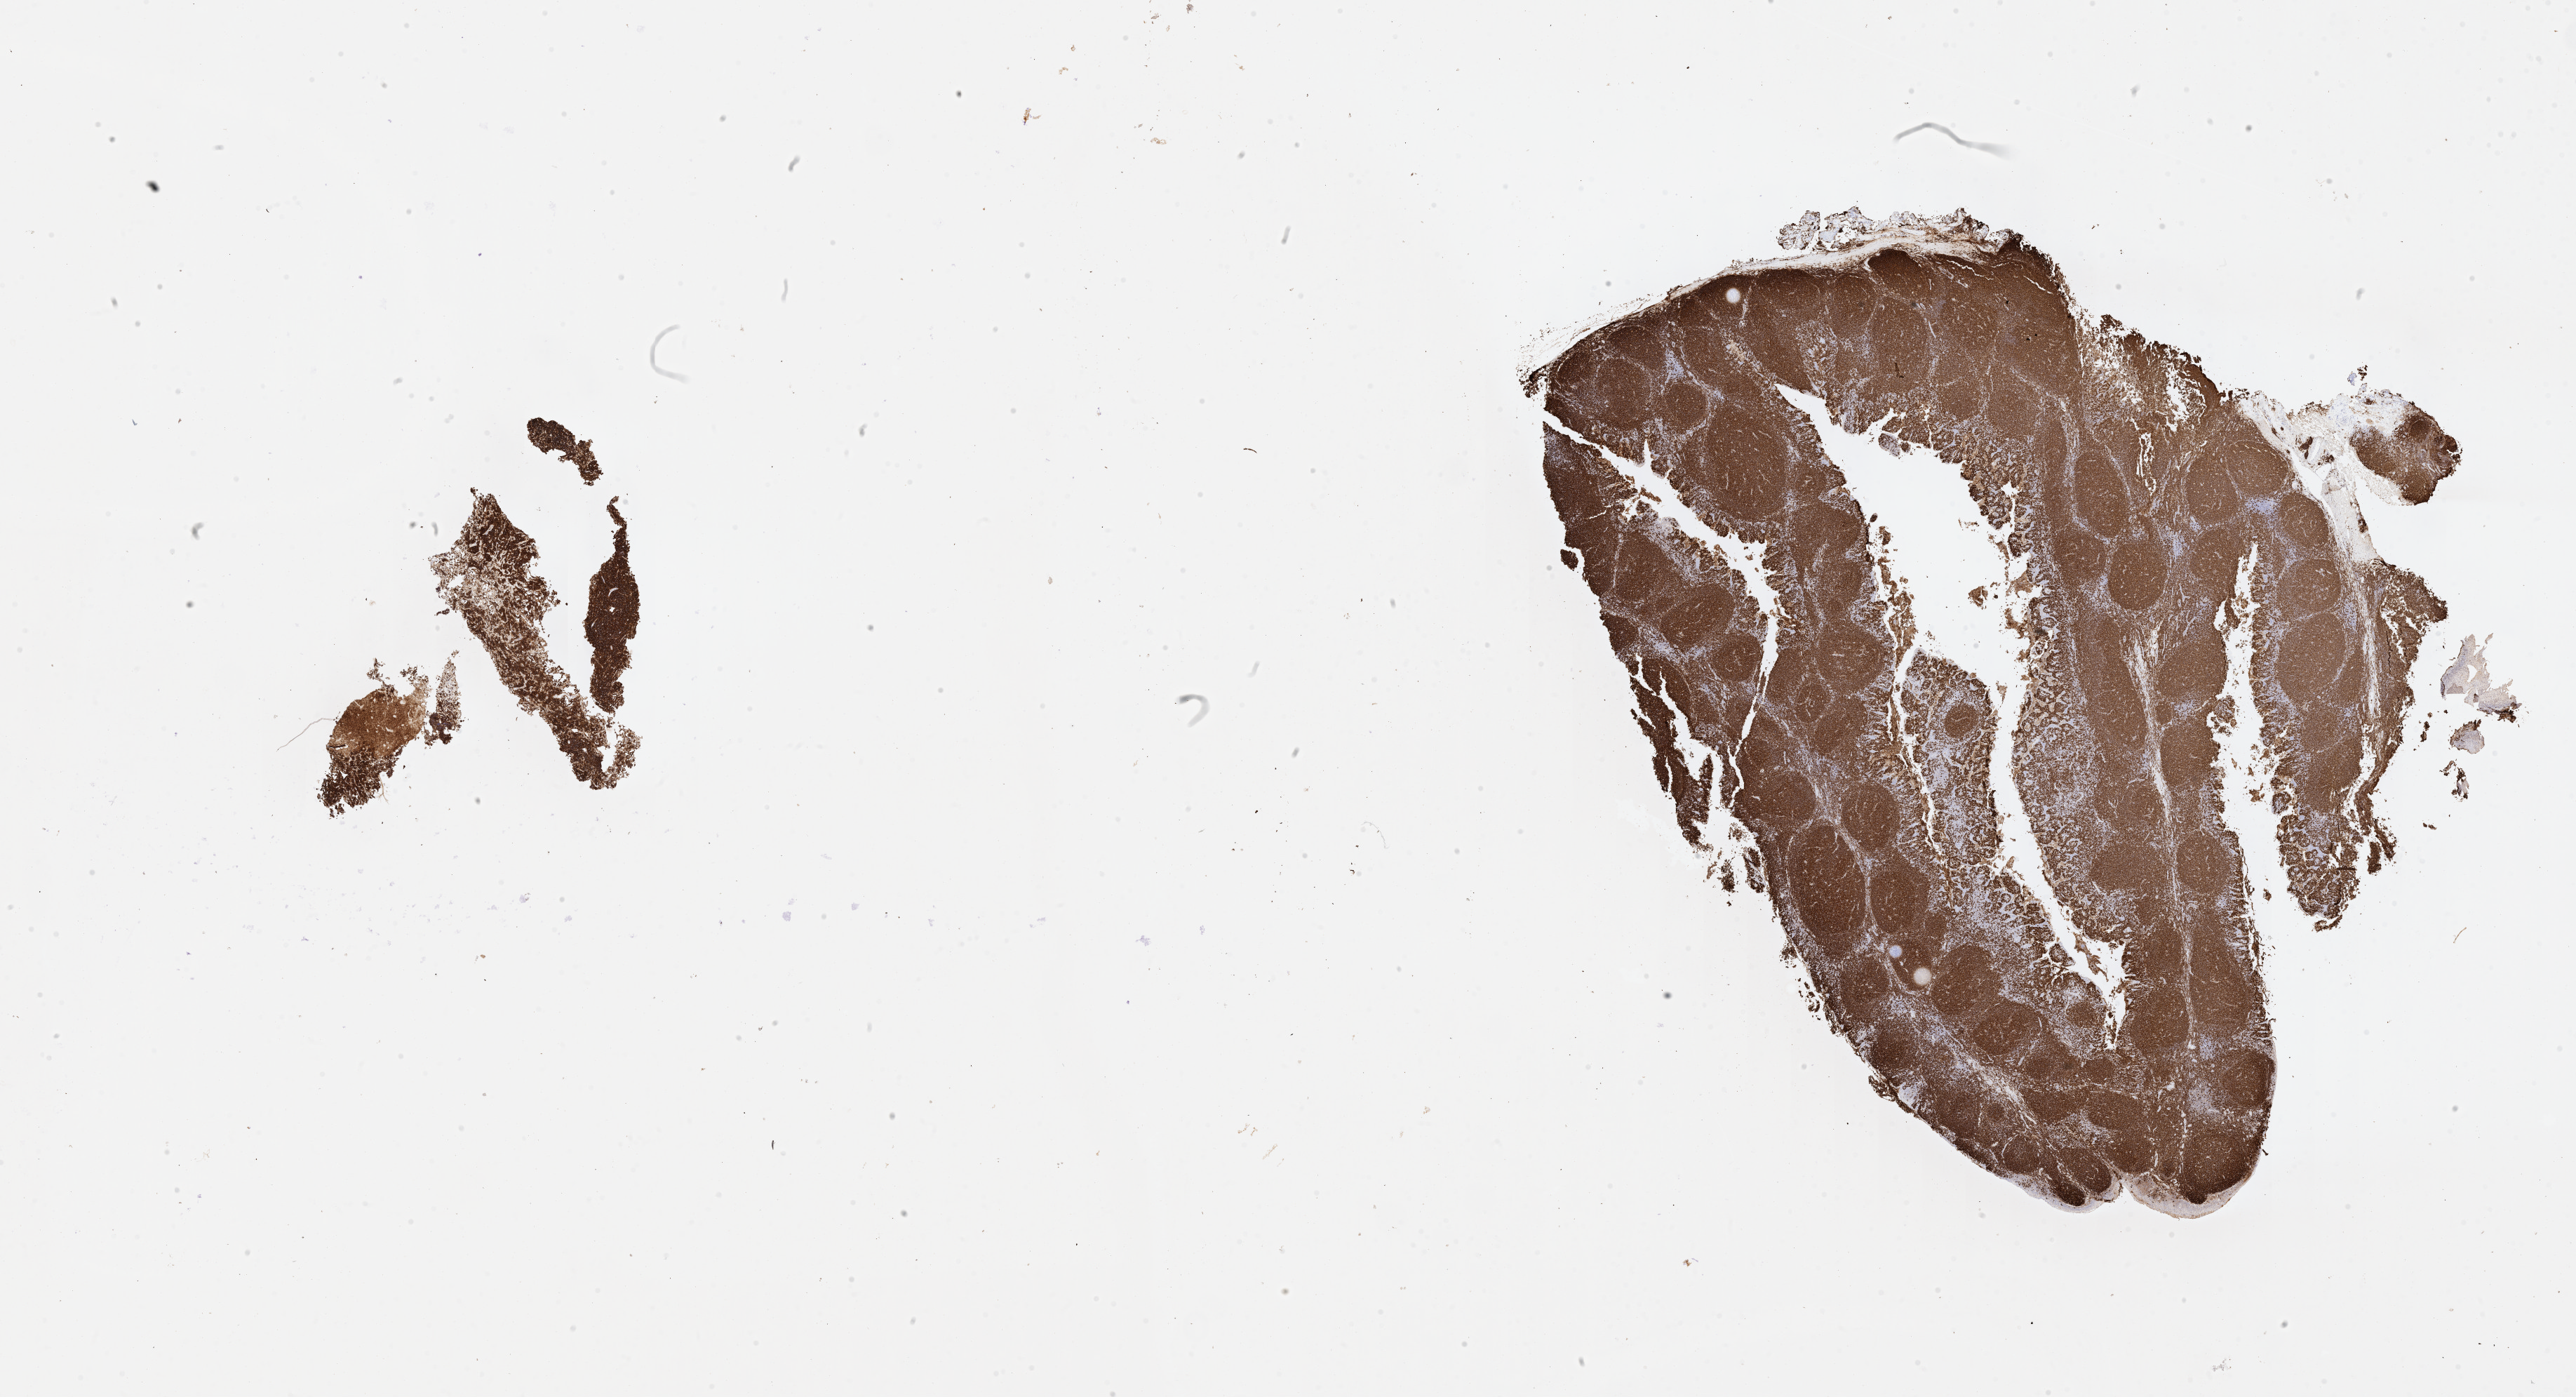
Whole-slide image, immunohistochemical stain for CD20, low-resolution overview of the scanned area, about 29.7 x 16.1 mm. Specimen: tumor tissue. Site: pelvis. Female patient; age at initial diagnosis 7 years.
Diagnosis: Burkitt lymphoma, NOS.